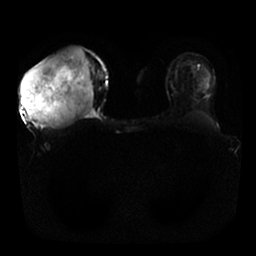
Breast MRI, one axial slice; position 13 of 25 along the scan axis; diffusion-weighted series; image 2 of 4 stored at this slice position (different b-values; order by instance number); 1.5 T; 256 × 256 image matrix, field of view 340 × 340 mm. Female patient.
Annotated regions visible in this slice (manually delineated by an expert):
- tumour on diffusion-weighted imaging: bounding box (x1, y1, x2, y2) in pixels: (21, 45, 93, 127)